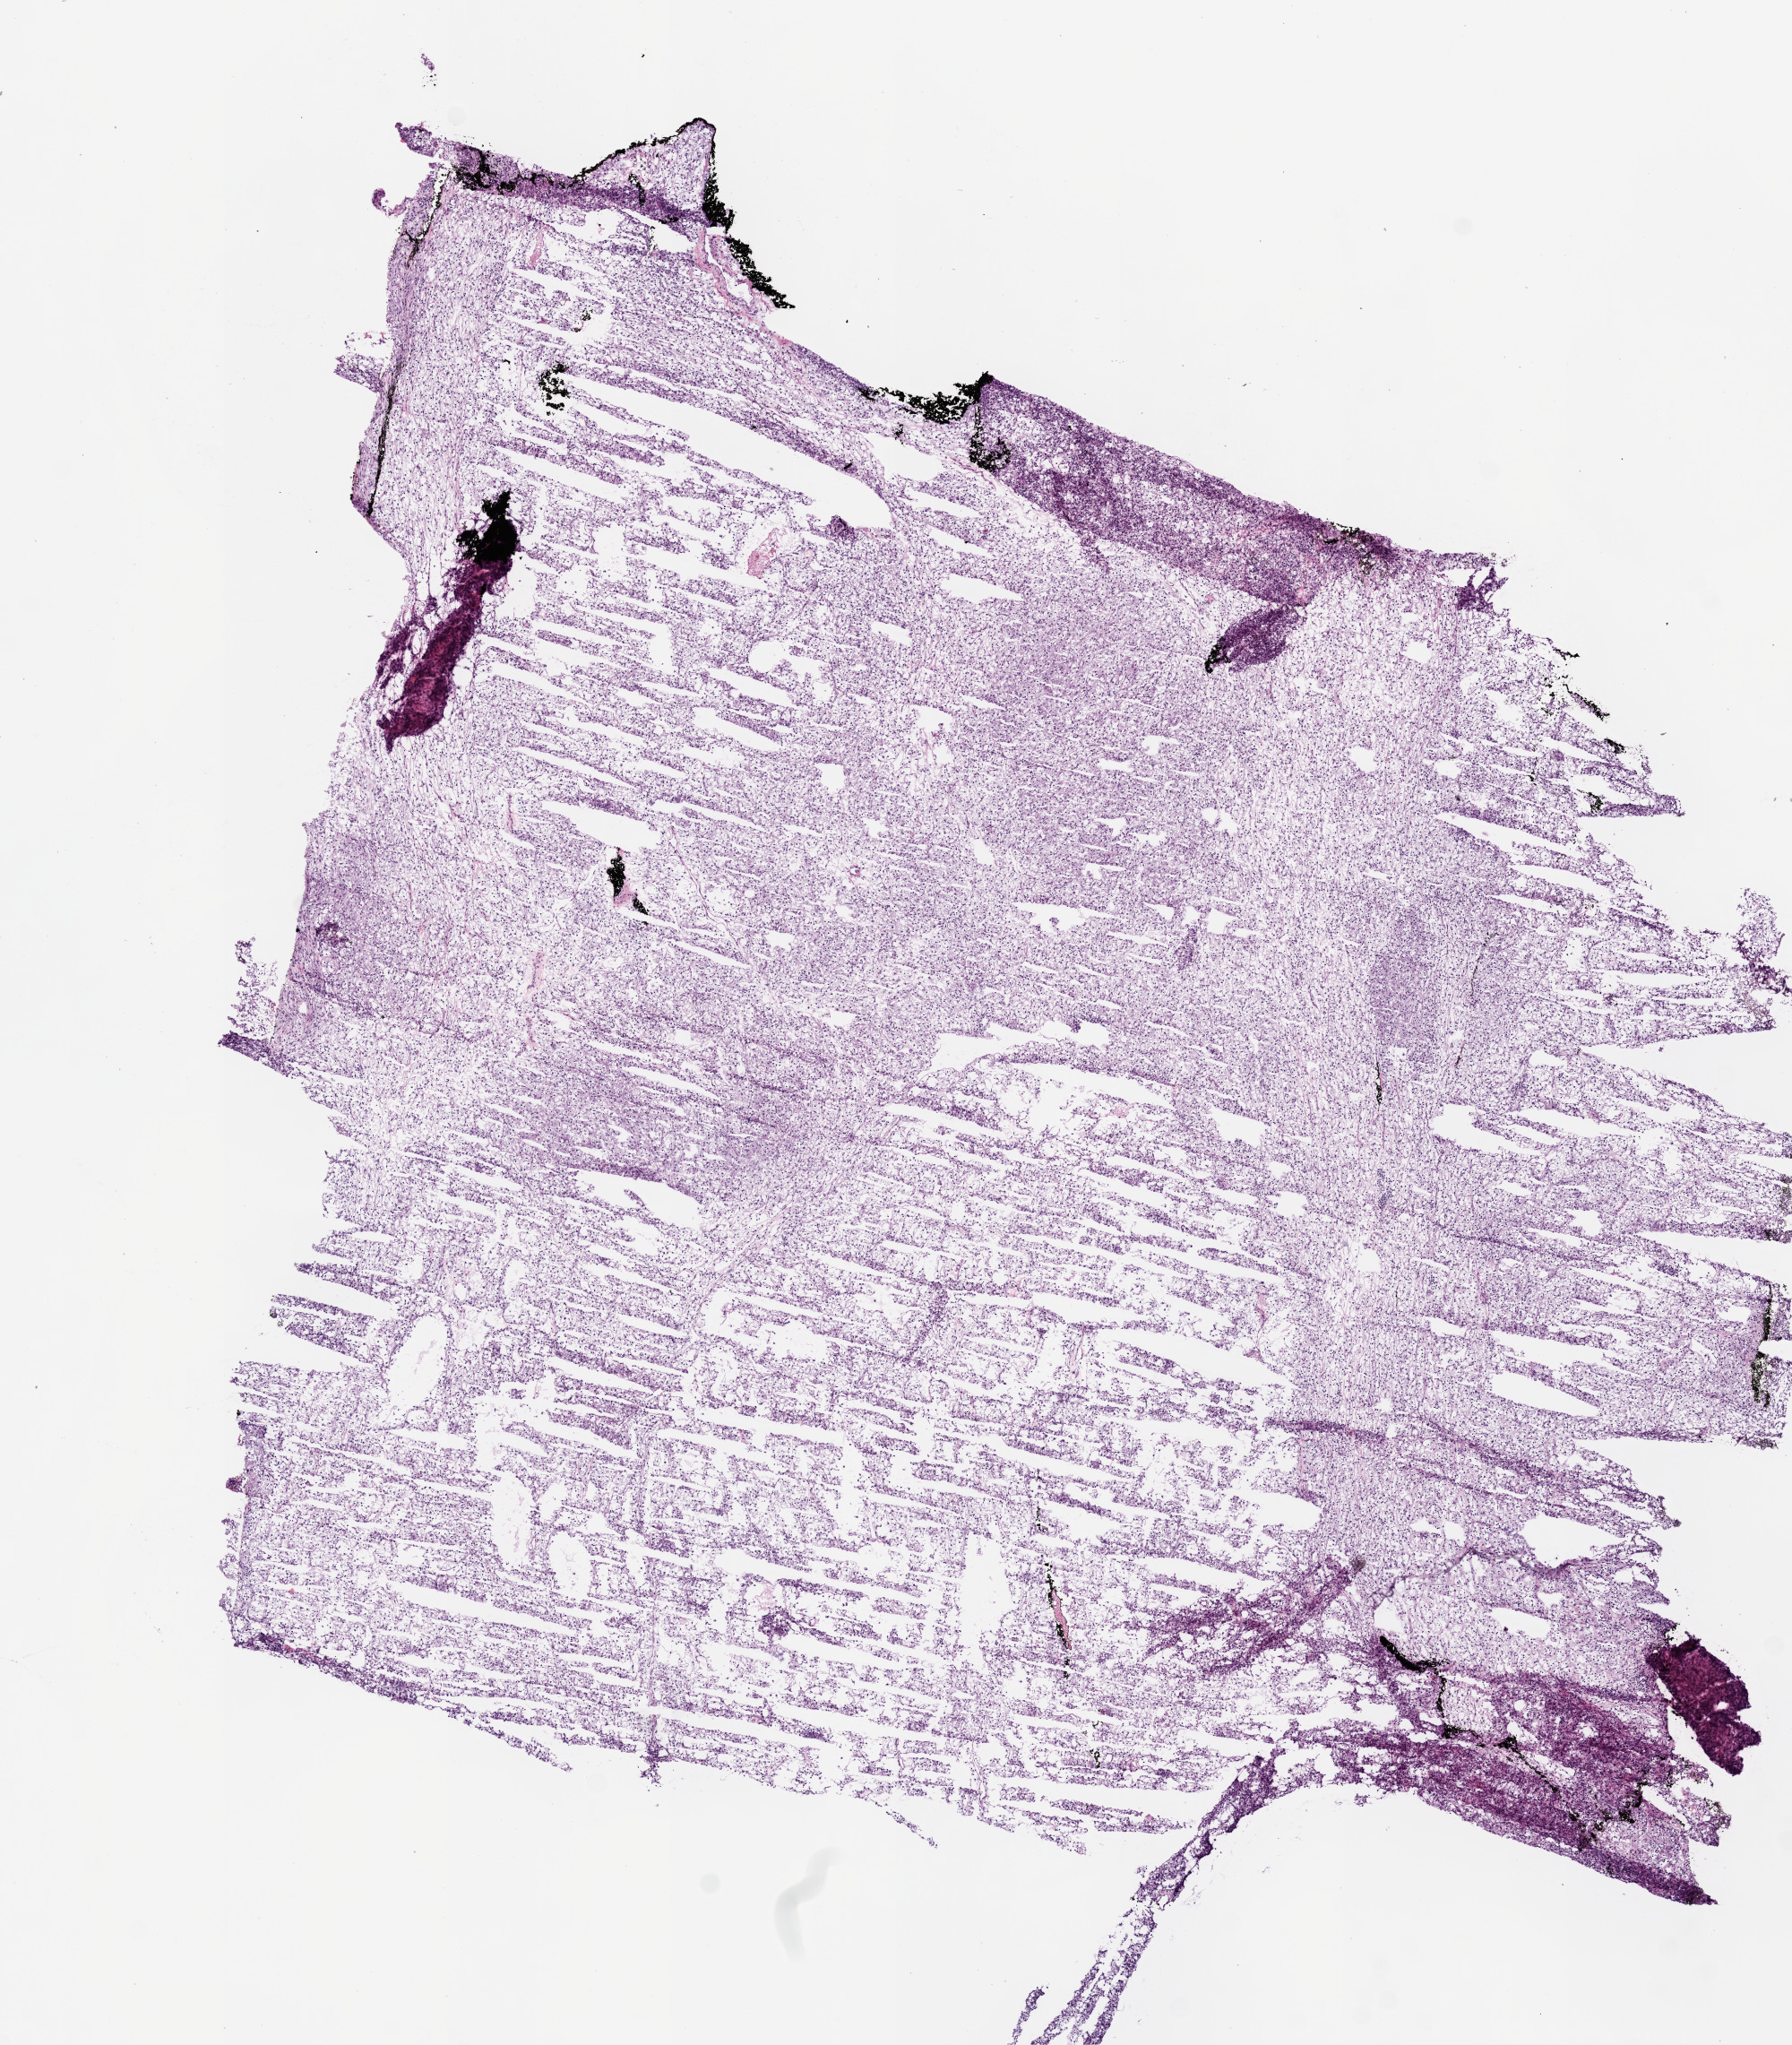
Whole-slide histology image, H&E-stained — low-resolution overview of the scanned area, about 8.0 x 9.2 mm (acquisition: 20x scan); frozen section from the top of the tissue portion; primary tumour sample from the kidney. Patient: male, age at initial diagnosis 57 years. Histologic grade: G2 (moderately differentiated). Composition of this section per pathologist review: tumour cells 95%, tumour nuclei 85%, normal cells 0%, stromal cells 5%, necrosis 0%.
Laterality: right. AJCC pathologic stage: I. Histologic diagnosis: Clear cell adenocarcinoma, NOS. TNM: T1 NX M0.